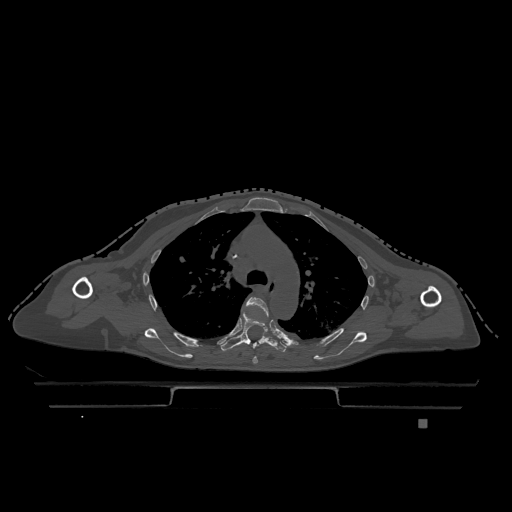
CT including the spine, one axial slice. Slice 852 of 1317 in the series (ordered by position). Bone window (W 1800 / L 400 HU). 0.5 mm slice thickness. 512 × 512 image matrix, field of view 500 × 500 mm. Patient: female, 74 years. Case-level facts recorded for this patient, not image findings: primary cancer: lung.
Outlined on this slice (semi-automatic segmentation, software-assisted and operator-edited):
- T4 vertebra: bounding box <245,297,269,364> (left, top, right, bottom; pixels)
- T5 vertebra: <221,311,288,352>